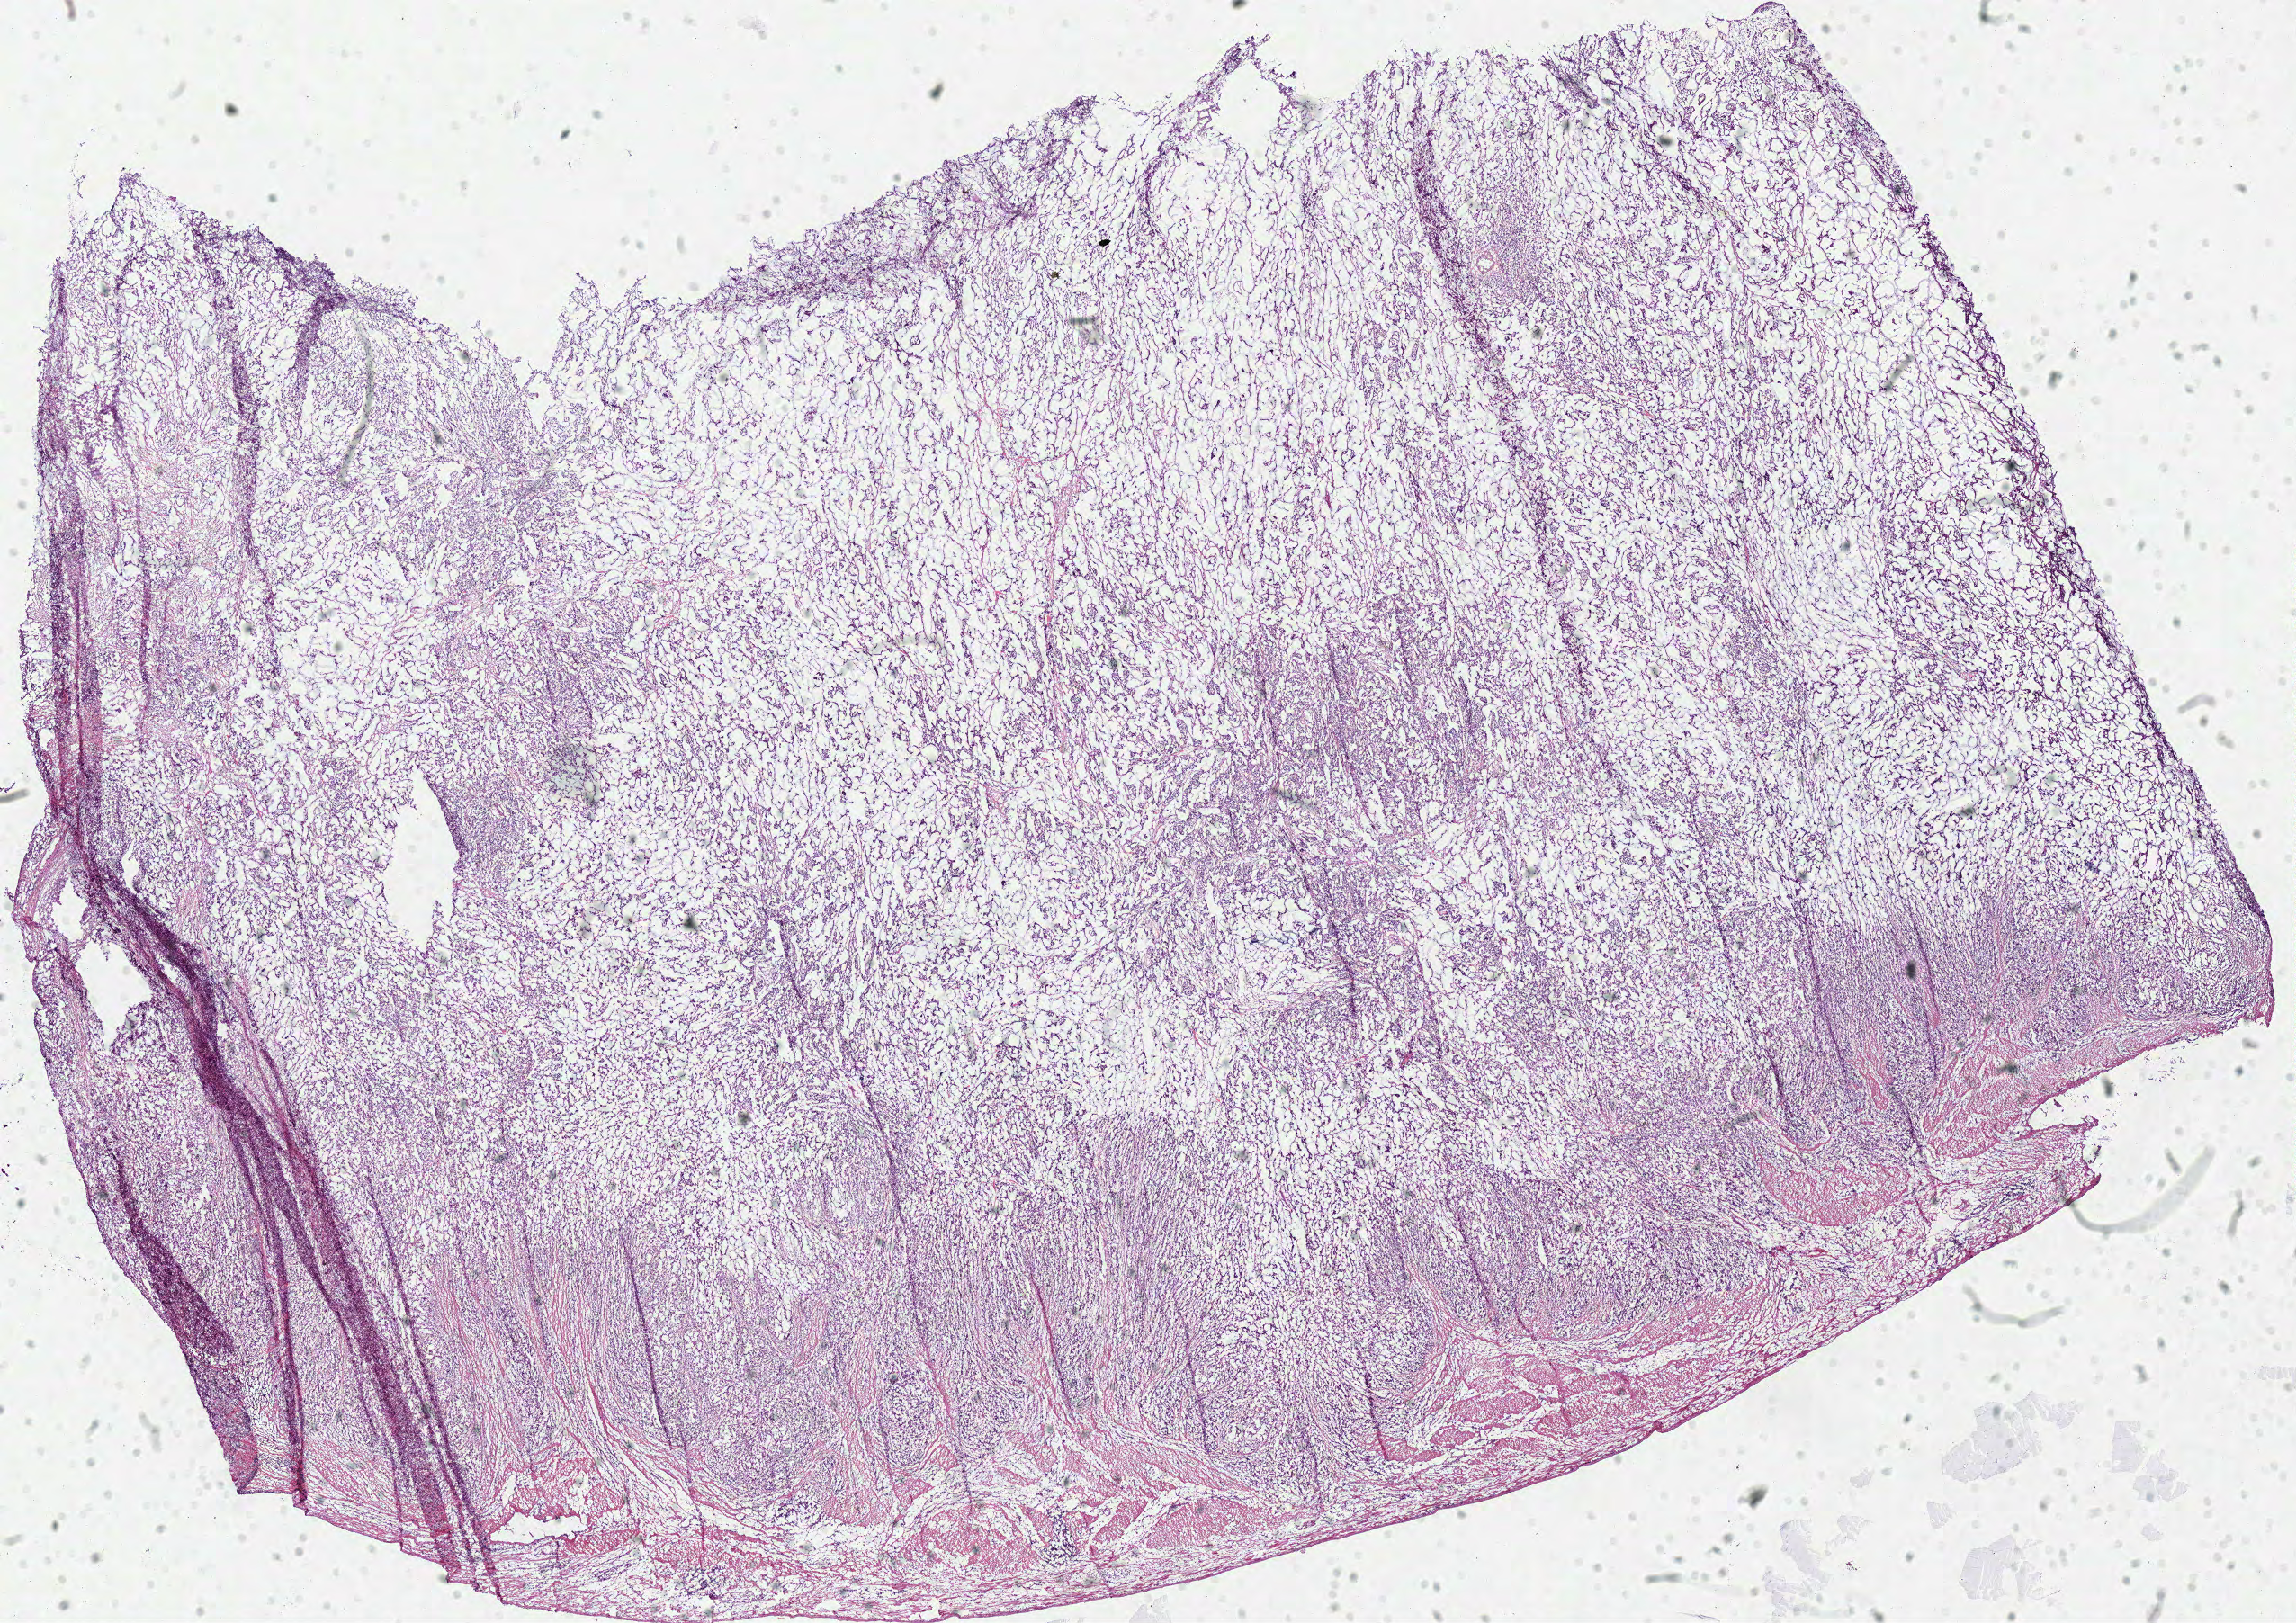
Digitized H&E-stained tissue section (whole slide), low-resolution overview of the scanned area, about 20.1 x 14.2 mm (slide scanned at 40x); frozen section from the bottom of the tissue portion; primary tumour sample from the stomach. Patient: female, age at initial diagnosis 64 years. Histologic grade: G3 (poorly differentiated). Pathologist review of this section (percent, as recorded): tumour cells 85%, tumour nuclei 80%, normal cells 0%, stromal cells 15%, necrosis 0%.
AJCC pathologic stage: IIA (7th edition). TNM: T3 N0 M0. Lymph nodes positive (case pathology): 0 of 3 examined. Pathologic diagnosis: Adenocarcinoma, NOS (body of stomach).